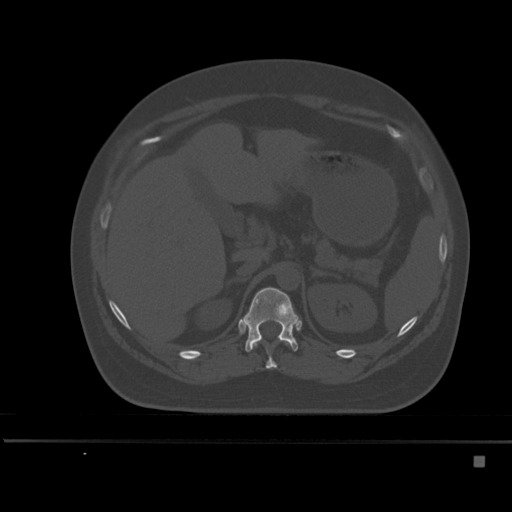
CT including the spine, one axial slice. Slice 219 of 495 in the series (ordered by position). Bone window (W 1800 / L 400 HU). 1.5 mm slice thickness. 512 × 512 image matrix, field of view 404 × 404 mm. Patient: female, 33 years. Case-level facts recorded for this patient, not image findings: primary cancer: breast; vertebrae with lytic lesions (as recorded): T1.
Outlined on this slice (semi-automatic segmentation, software-assisted and operator-edited):
- T11 vertebra: bounding box (x1, y1, x2, y2) in pixels: (252, 342, 290, 369)
- T12 vertebra: (243, 287, 298, 352)